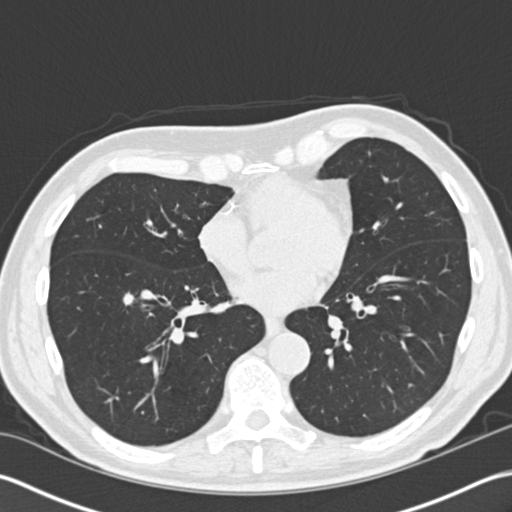
Chest CT (low-dose screening protocol), one axial image, baseline annual screen, lung window (W 1500 / L -600 HU), standard (soft-tissue) reconstruction kernel (B30f), slice 100 of 168 in the series, 512 × 512 image matrix. Male, age 73 years at enrolment. Former smoker at enrolment.
Expert reader's lesion annotation, bounding box [x1, y1, x2, y2] px = [99, 278, 150, 322]. No non-calcified nodule or mass ≥4 mm was recorded by the screening reader at this exam. Later outcome: lung cancer diagnosed 430 days after this screen — non-small cell carcinoma, right lower lobe, stage IA (AJCC 6th edition), 30 mm at pathology.